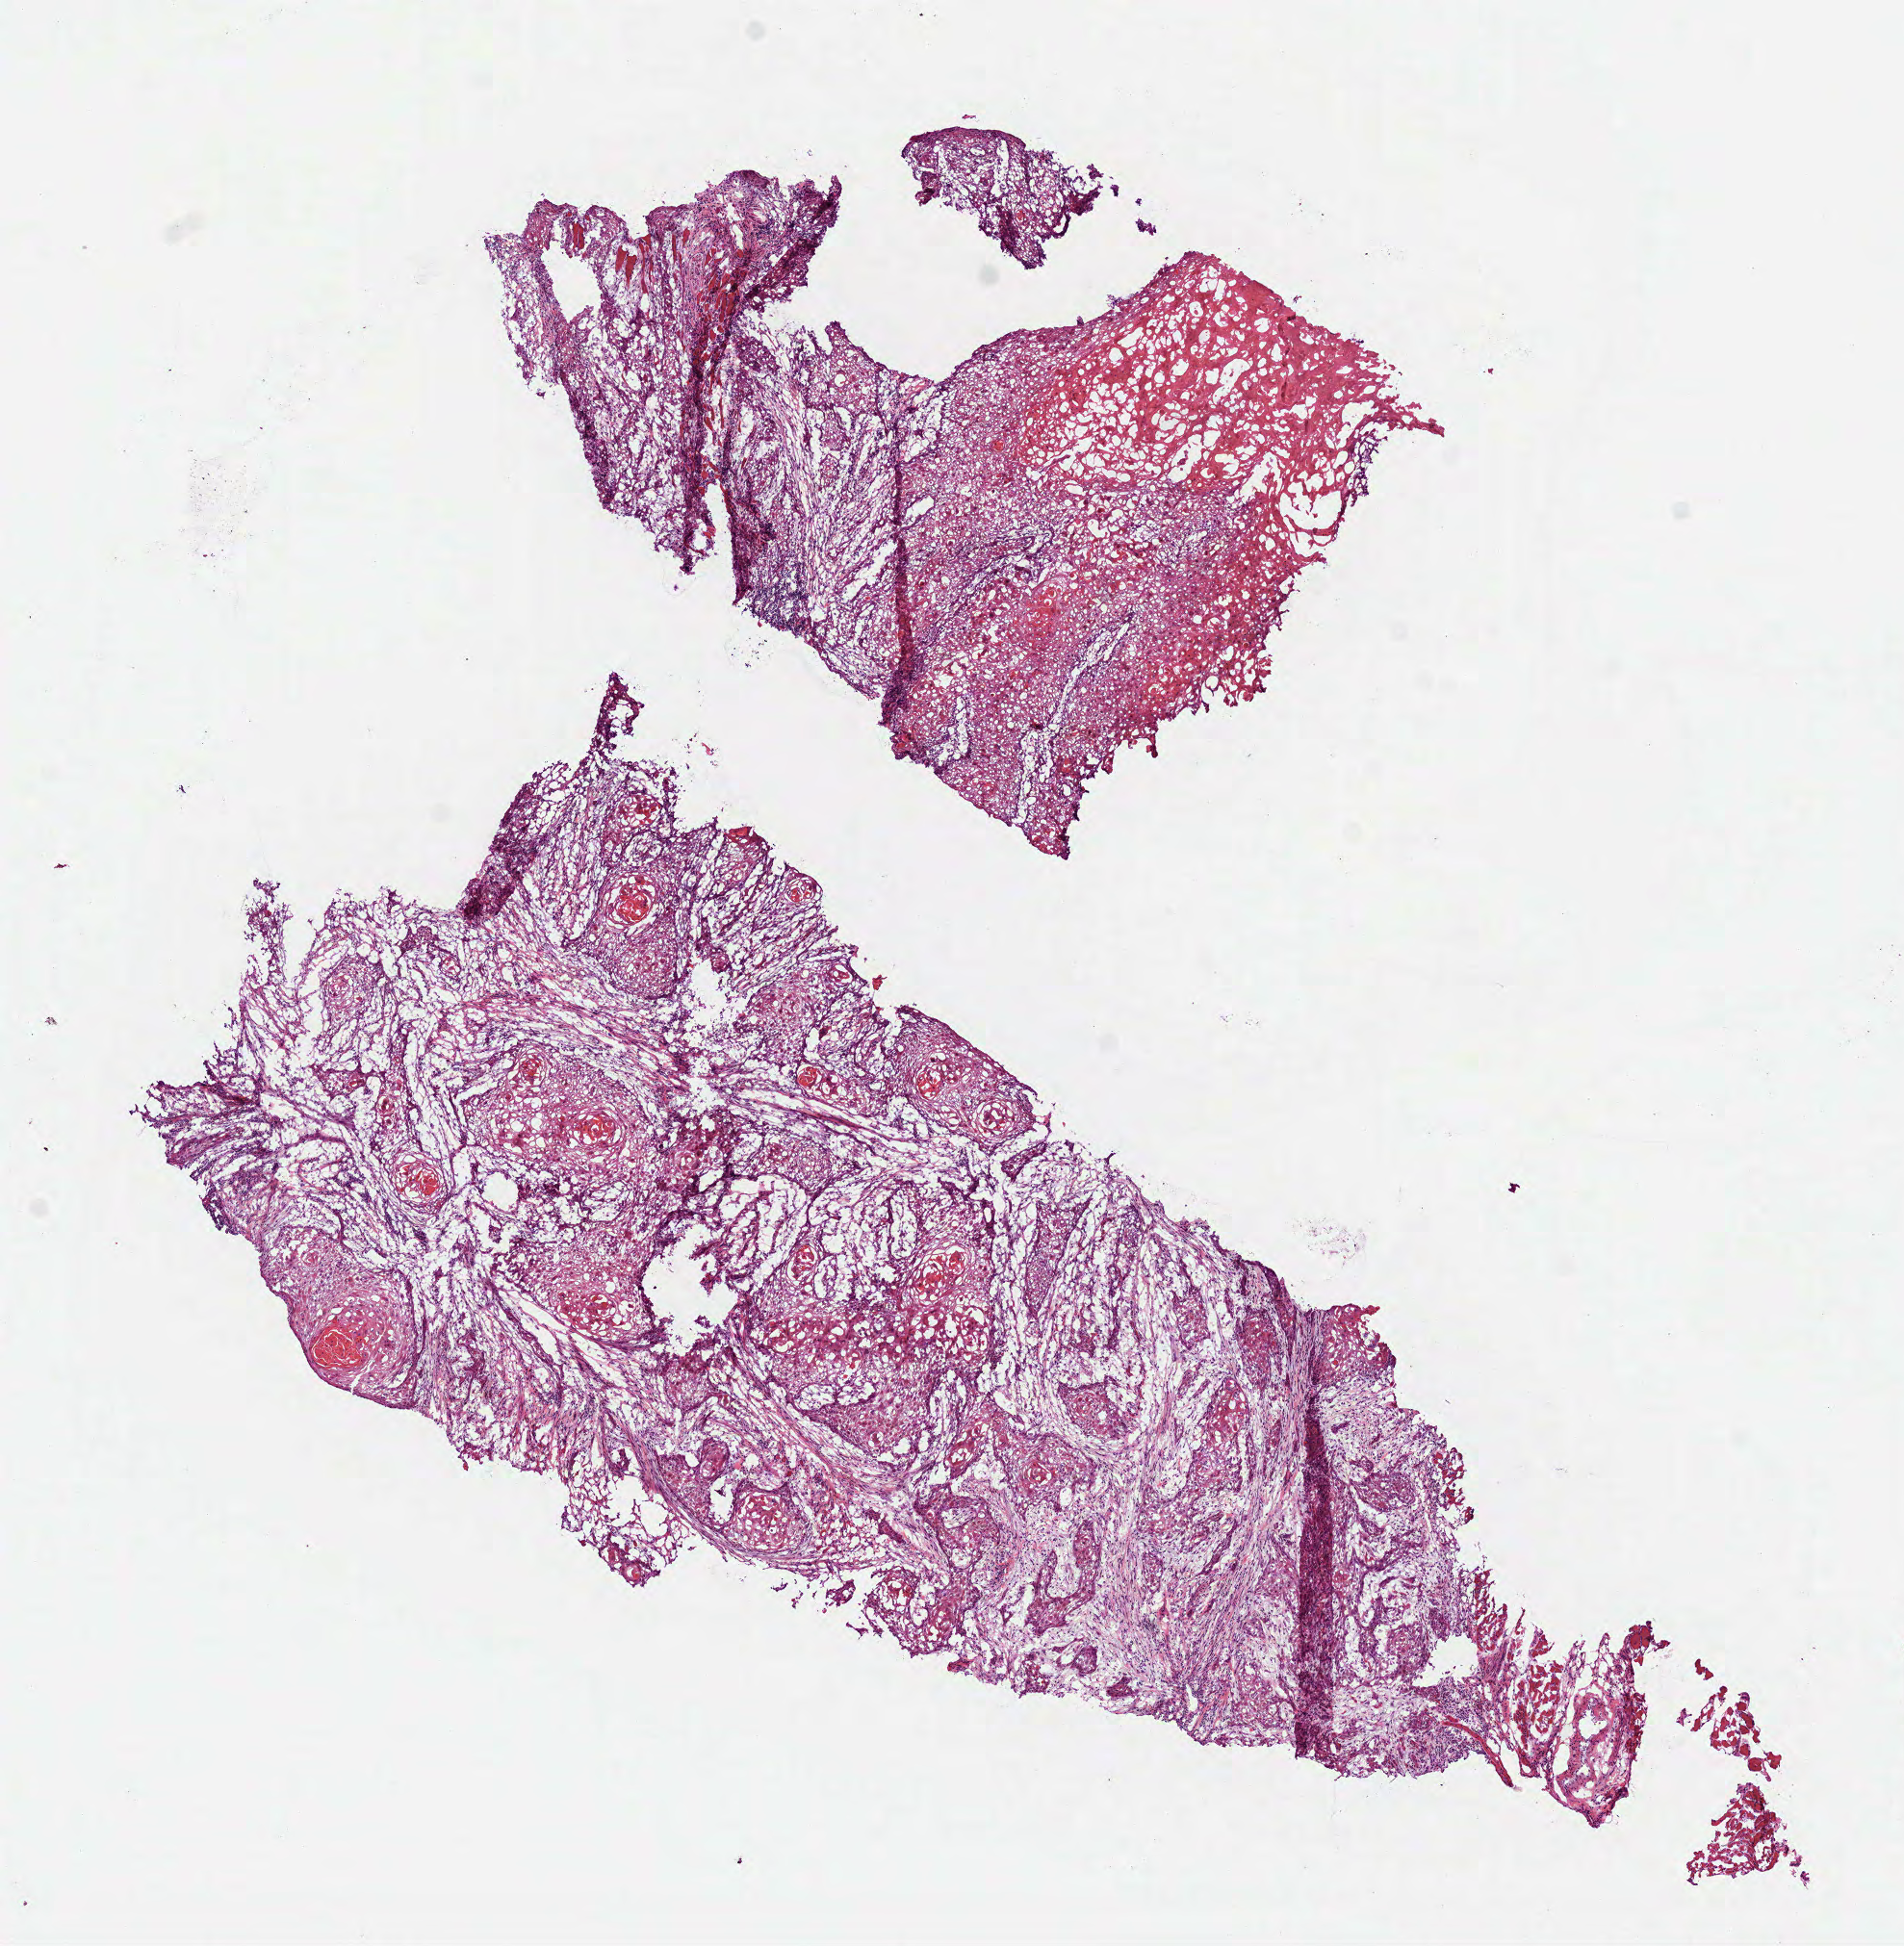
Hematoxylin and eosin (H&E) stained whole-slide image — low-resolution overview of the scanned area, about 8.0 x 8.2 mm, frozen section from the bottom of the tissue portion, head and neck, primary tumour sample. Patient: female, age at initial diagnosis 69 years. Histologic grade: G2 (moderately differentiated). Pathologist review of this section (percent, as recorded): tumour cells 85%, tumour nuclei 75%, normal cells 0%, stromal cells 15%, necrosis 0%.
* laterality: left
* AJCC pathologic stage: II
* histologic diagnosis: Squamous cell carcinoma, NOS (tongue, NOS)